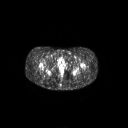
FDG PET of an extremity soft-tissue mass (from a PET/CT study), one axial slice. Slice 36 of 267 in the series (ordered by position). 3.27 mm slice thickness. 128 × 128 image matrix, field of view 700 × 700 mm. Patient: female, 17 years. Case-level facts recorded for this patient, not image findings: histological type: epithelioid sarcoma; grade: intermediate; site of the primary tumour: right buttock.
Outlined on this slice (expert contour drawn on MRI and transferred to this co-registered scan by the dataset authors):
- gross tumour volume including surrounding oedema: bounding box (x1, y1, x2, y2) in pixels: (51, 71, 57, 77)